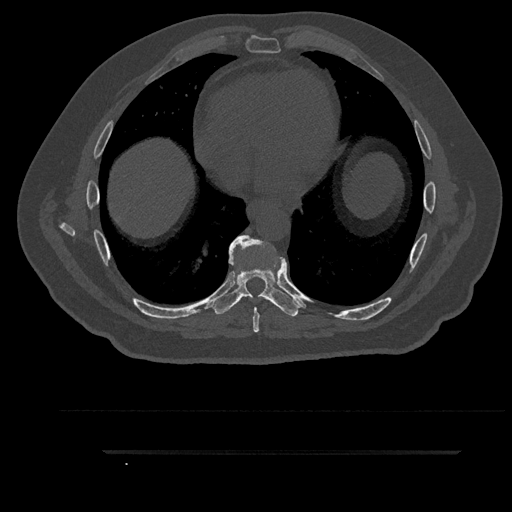
CT including the spine, one axial slice. Position 495 of 797 along the scan axis. Bone window (W 1800 / L 400 HU). 0.5 mm slice thickness. 512 × 512 image matrix, field of view 432 × 432 mm. Male patient, age 63 years. From the clinical record (not read from this slice): primary cancer: renal; vertebrae with lytic lesions (as recorded): T8.
Outlined on this slice (semi-automatically segmented with operator editing):
- T7 vertebra: bounding box (x1, y1, x2, y2) in pixels: (229, 235, 285, 332)
- T8 vertebra: (212, 235, 301, 316)